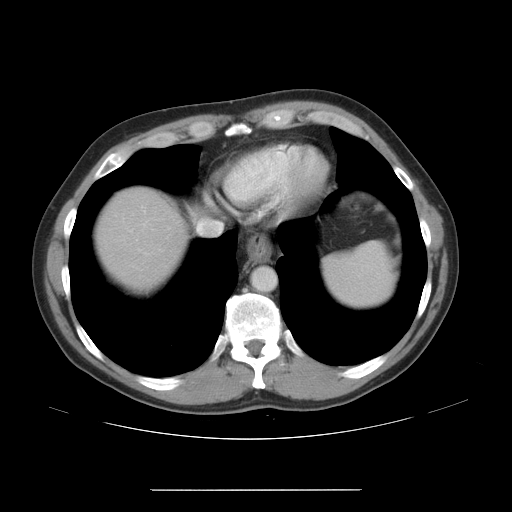
Contrast-enhanced abdominal CT, one axial slice. Position 40 of 48 along the scan axis. Intravenous contrast given. Soft-tissue window (W 400 / L 40 HU). 5 mm slice thickness. 512 × 512 image matrix, field of view 409 × 409 mm. Male patient, age 56 years. From the clinical record (not read from this slice): diagnosis: colorectal cancer liver metastases, imaged before liver resection; multiple liver metastases: yes.
Structures marked on this image (outlined manually by an expert reader):
- hepatic veins: bounding box <197,222,222,234> (left, top, right, bottom; pixels)
- liver: <98,191,183,289>
- planned liver remnant (the part of the liver to remain after resection): <98,191,183,289>